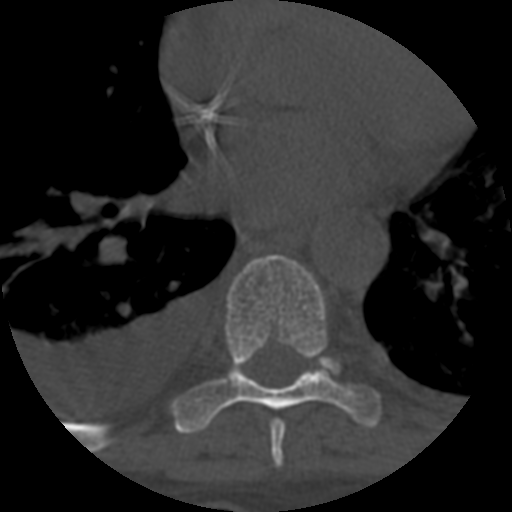
CT including the spine, one axial slice; position 398 of 708 along the scan axis; reconstruction kernel STANDARD; 120 kVp; one of 3 acquisitions stored at this slice position; bone window (W 1800 / L 400 HU); 1.25 mm slice thickness; 512 × 512 image matrix, field of view 160 × 160 mm. Patient age 55 years. From the clinical record (not read from this slice): primary cancer: colon.
Outlined on this slice (semi-automatic segmentation, software-assisted and operator-edited):
- T7 vertebra: bounding box [x1, y1, x2, y2] px = [270, 420, 286, 466]
- T8 vertebra: [174, 254, 380, 434]
- T9 vertebra: [321, 357, 341, 376]